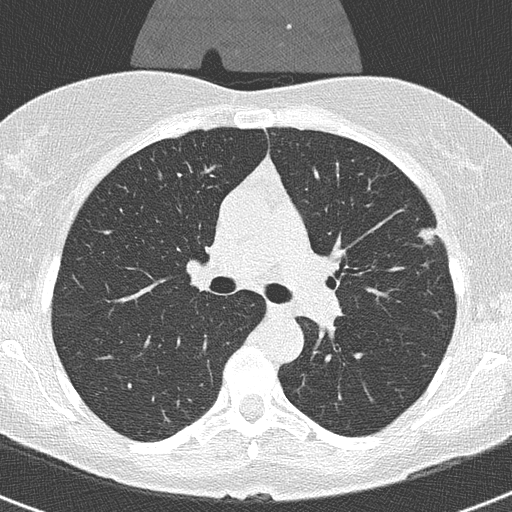
Low-dose screening chest CT, one axial slice; slice 211 of 320 in the series (ordered by position); reconstruction kernel B50f; 120 kVp; lung window (W 1500 / L -600 HU); 2 mm slice thickness; 512 × 512 image matrix, field of view 290 × 290 mm.
Annotated regions visible in this slice (manually delineated by an expert):
- lesion 1 (tumor, upper lobe of left lung): bounding box <418,228,435,245> (left, top, right, bottom; pixels)